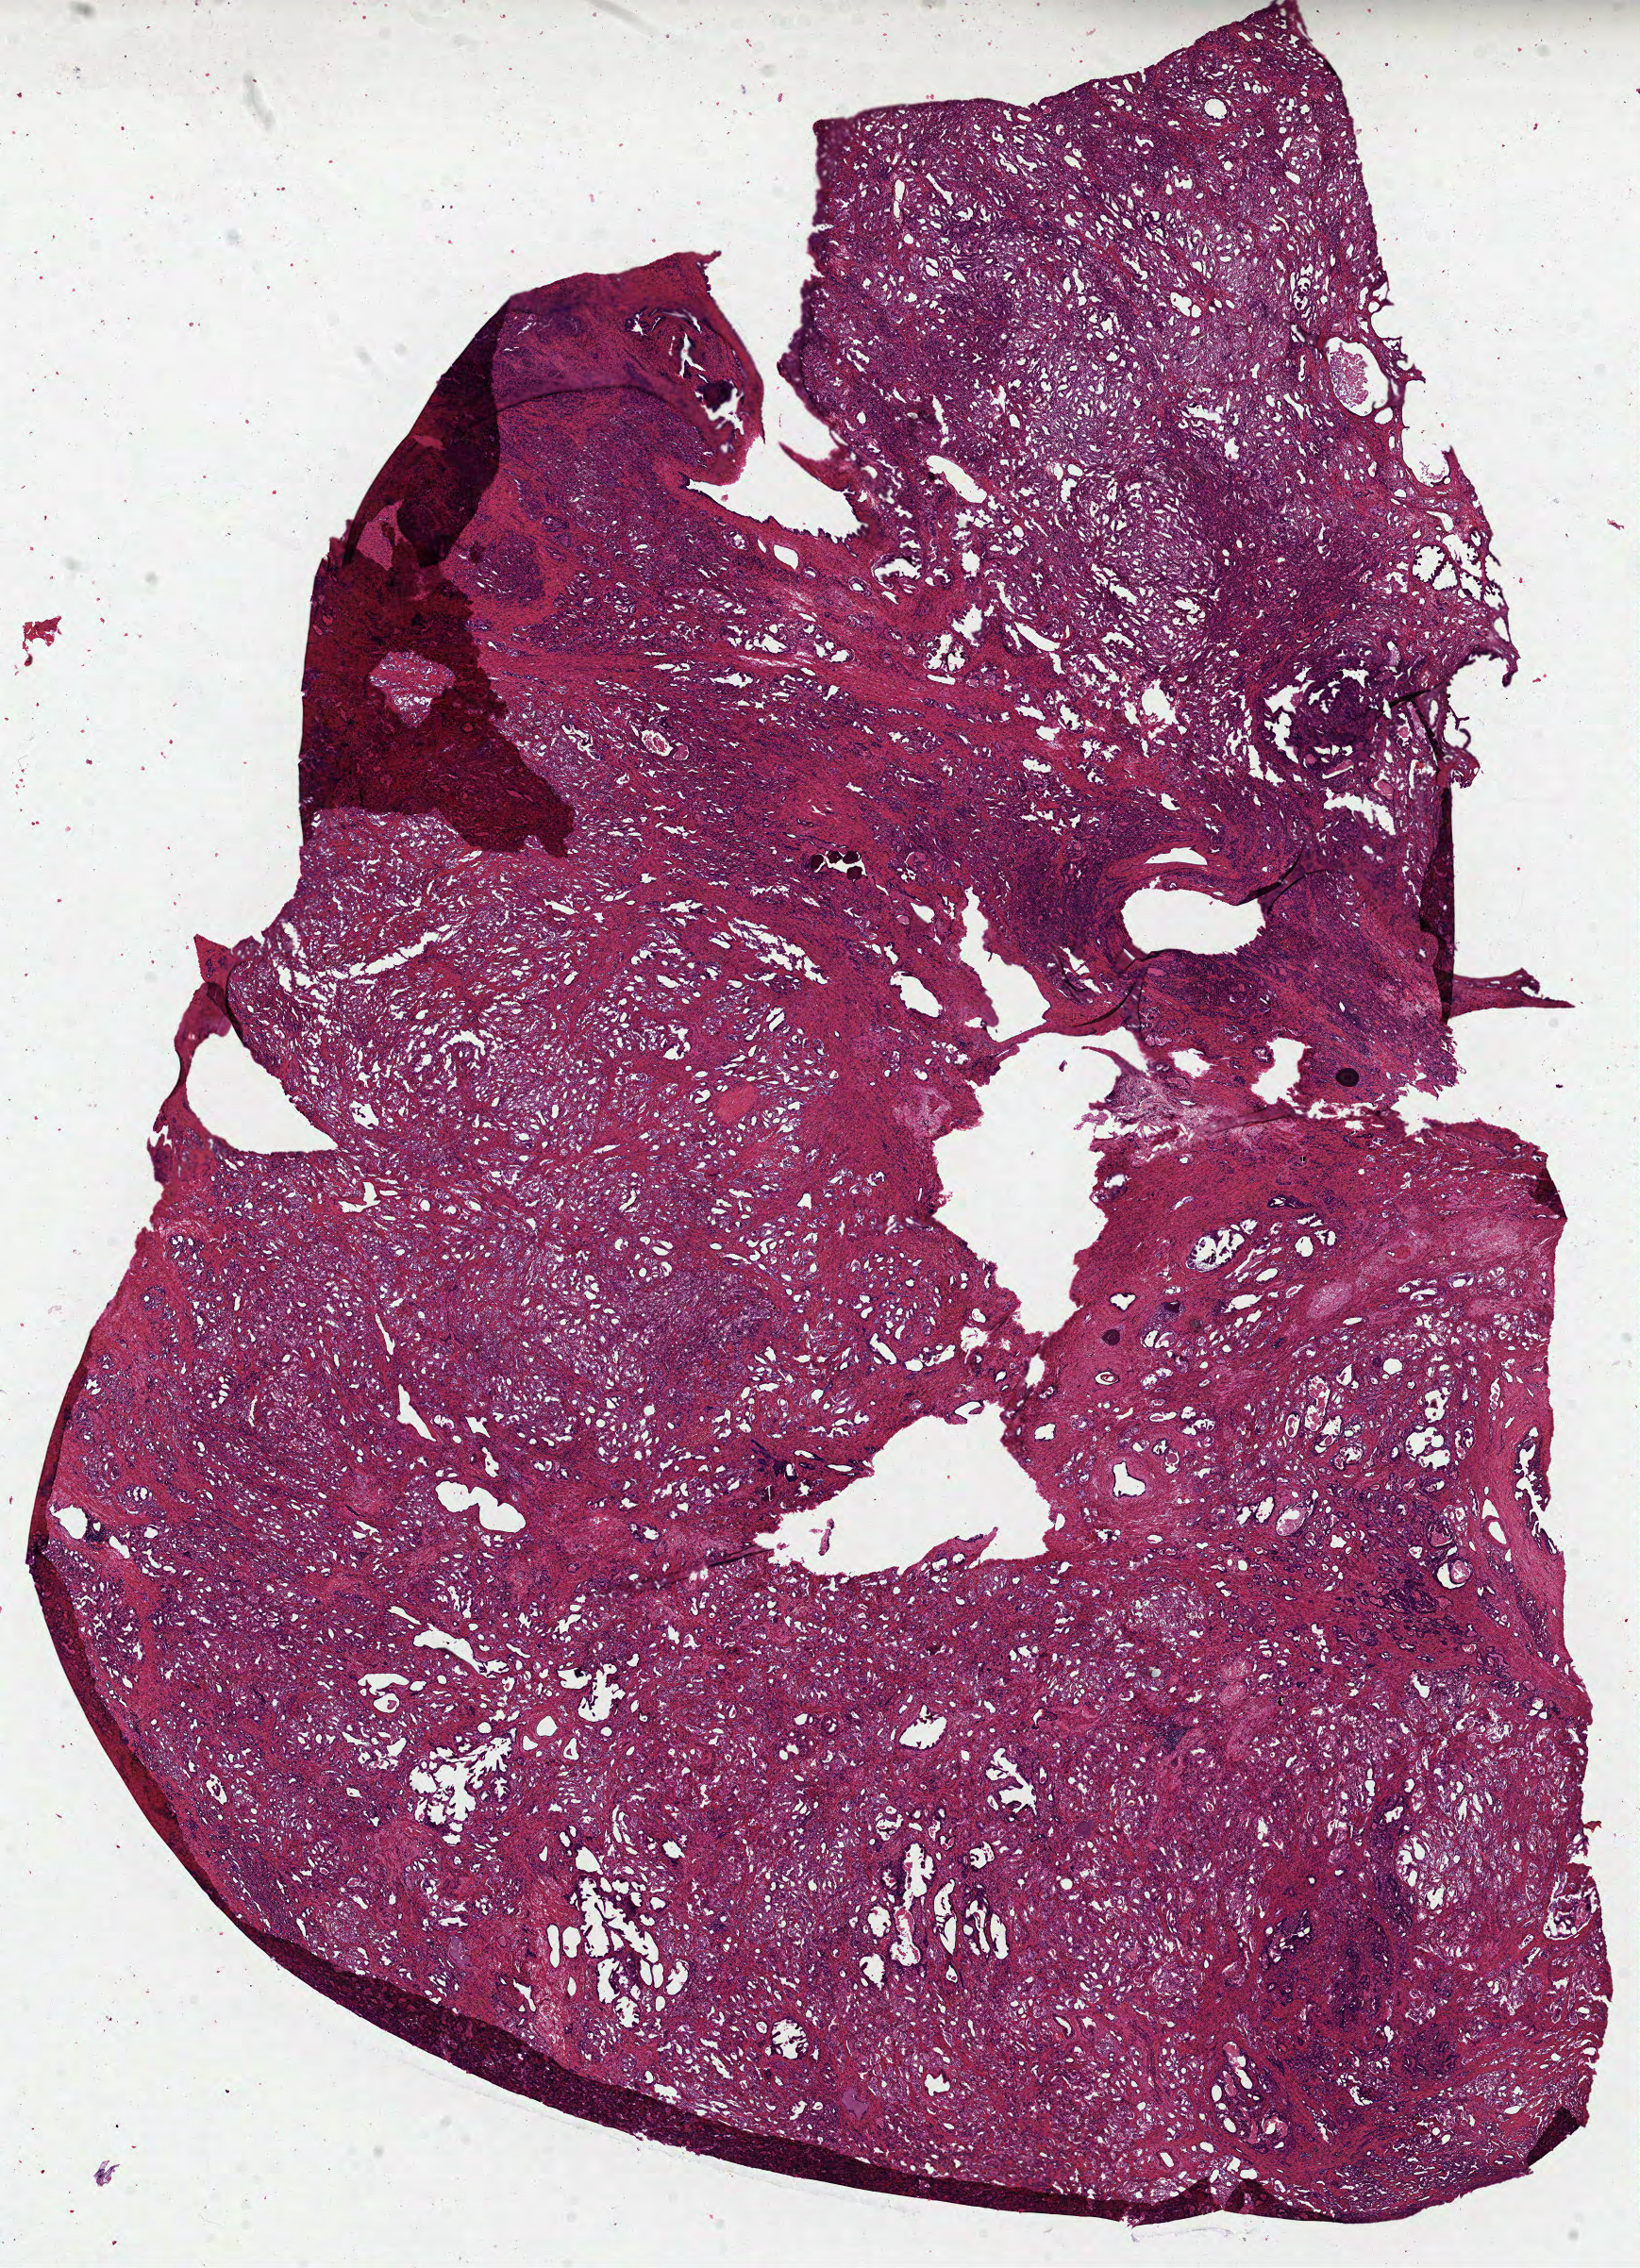
Whole-slide histology image, H&E — whole scanned area (about 14.0 x 19.4 mm) shown as a low-resolution overview, formalin-fixed paraffin-embedded (FFPE) diagnostic section, primary tumour sample from the prostate. Patient: male, age at initial diagnosis 65 years.
Diagnosis: Acinar cell carcinoma (prostate gland).